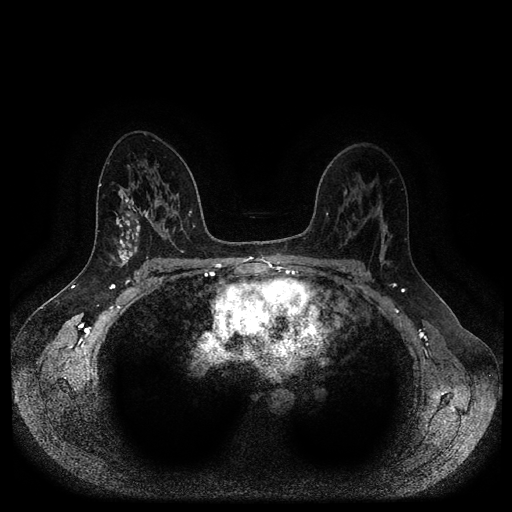
Breast MRI (dynamic contrast-enhanced, multi-phase), one axial slice; position 62 of 116 along the scan axis; dynamic contrast-enhanced series, time point 2 of 5 at this slice position (early post-contrast); 1.5 T; TE 2.6 ms, TR 5.3 ms; 2 mm slice thickness; 512 × 512 image matrix, field of view 360 × 360 mm. Female patient, age 45 years.
Outlined on this slice (semi-automatically segmented with operator editing):
- breast lesion (labelled benign in the annotation): box from (x=112, y=189) to (x=142, y=267) px